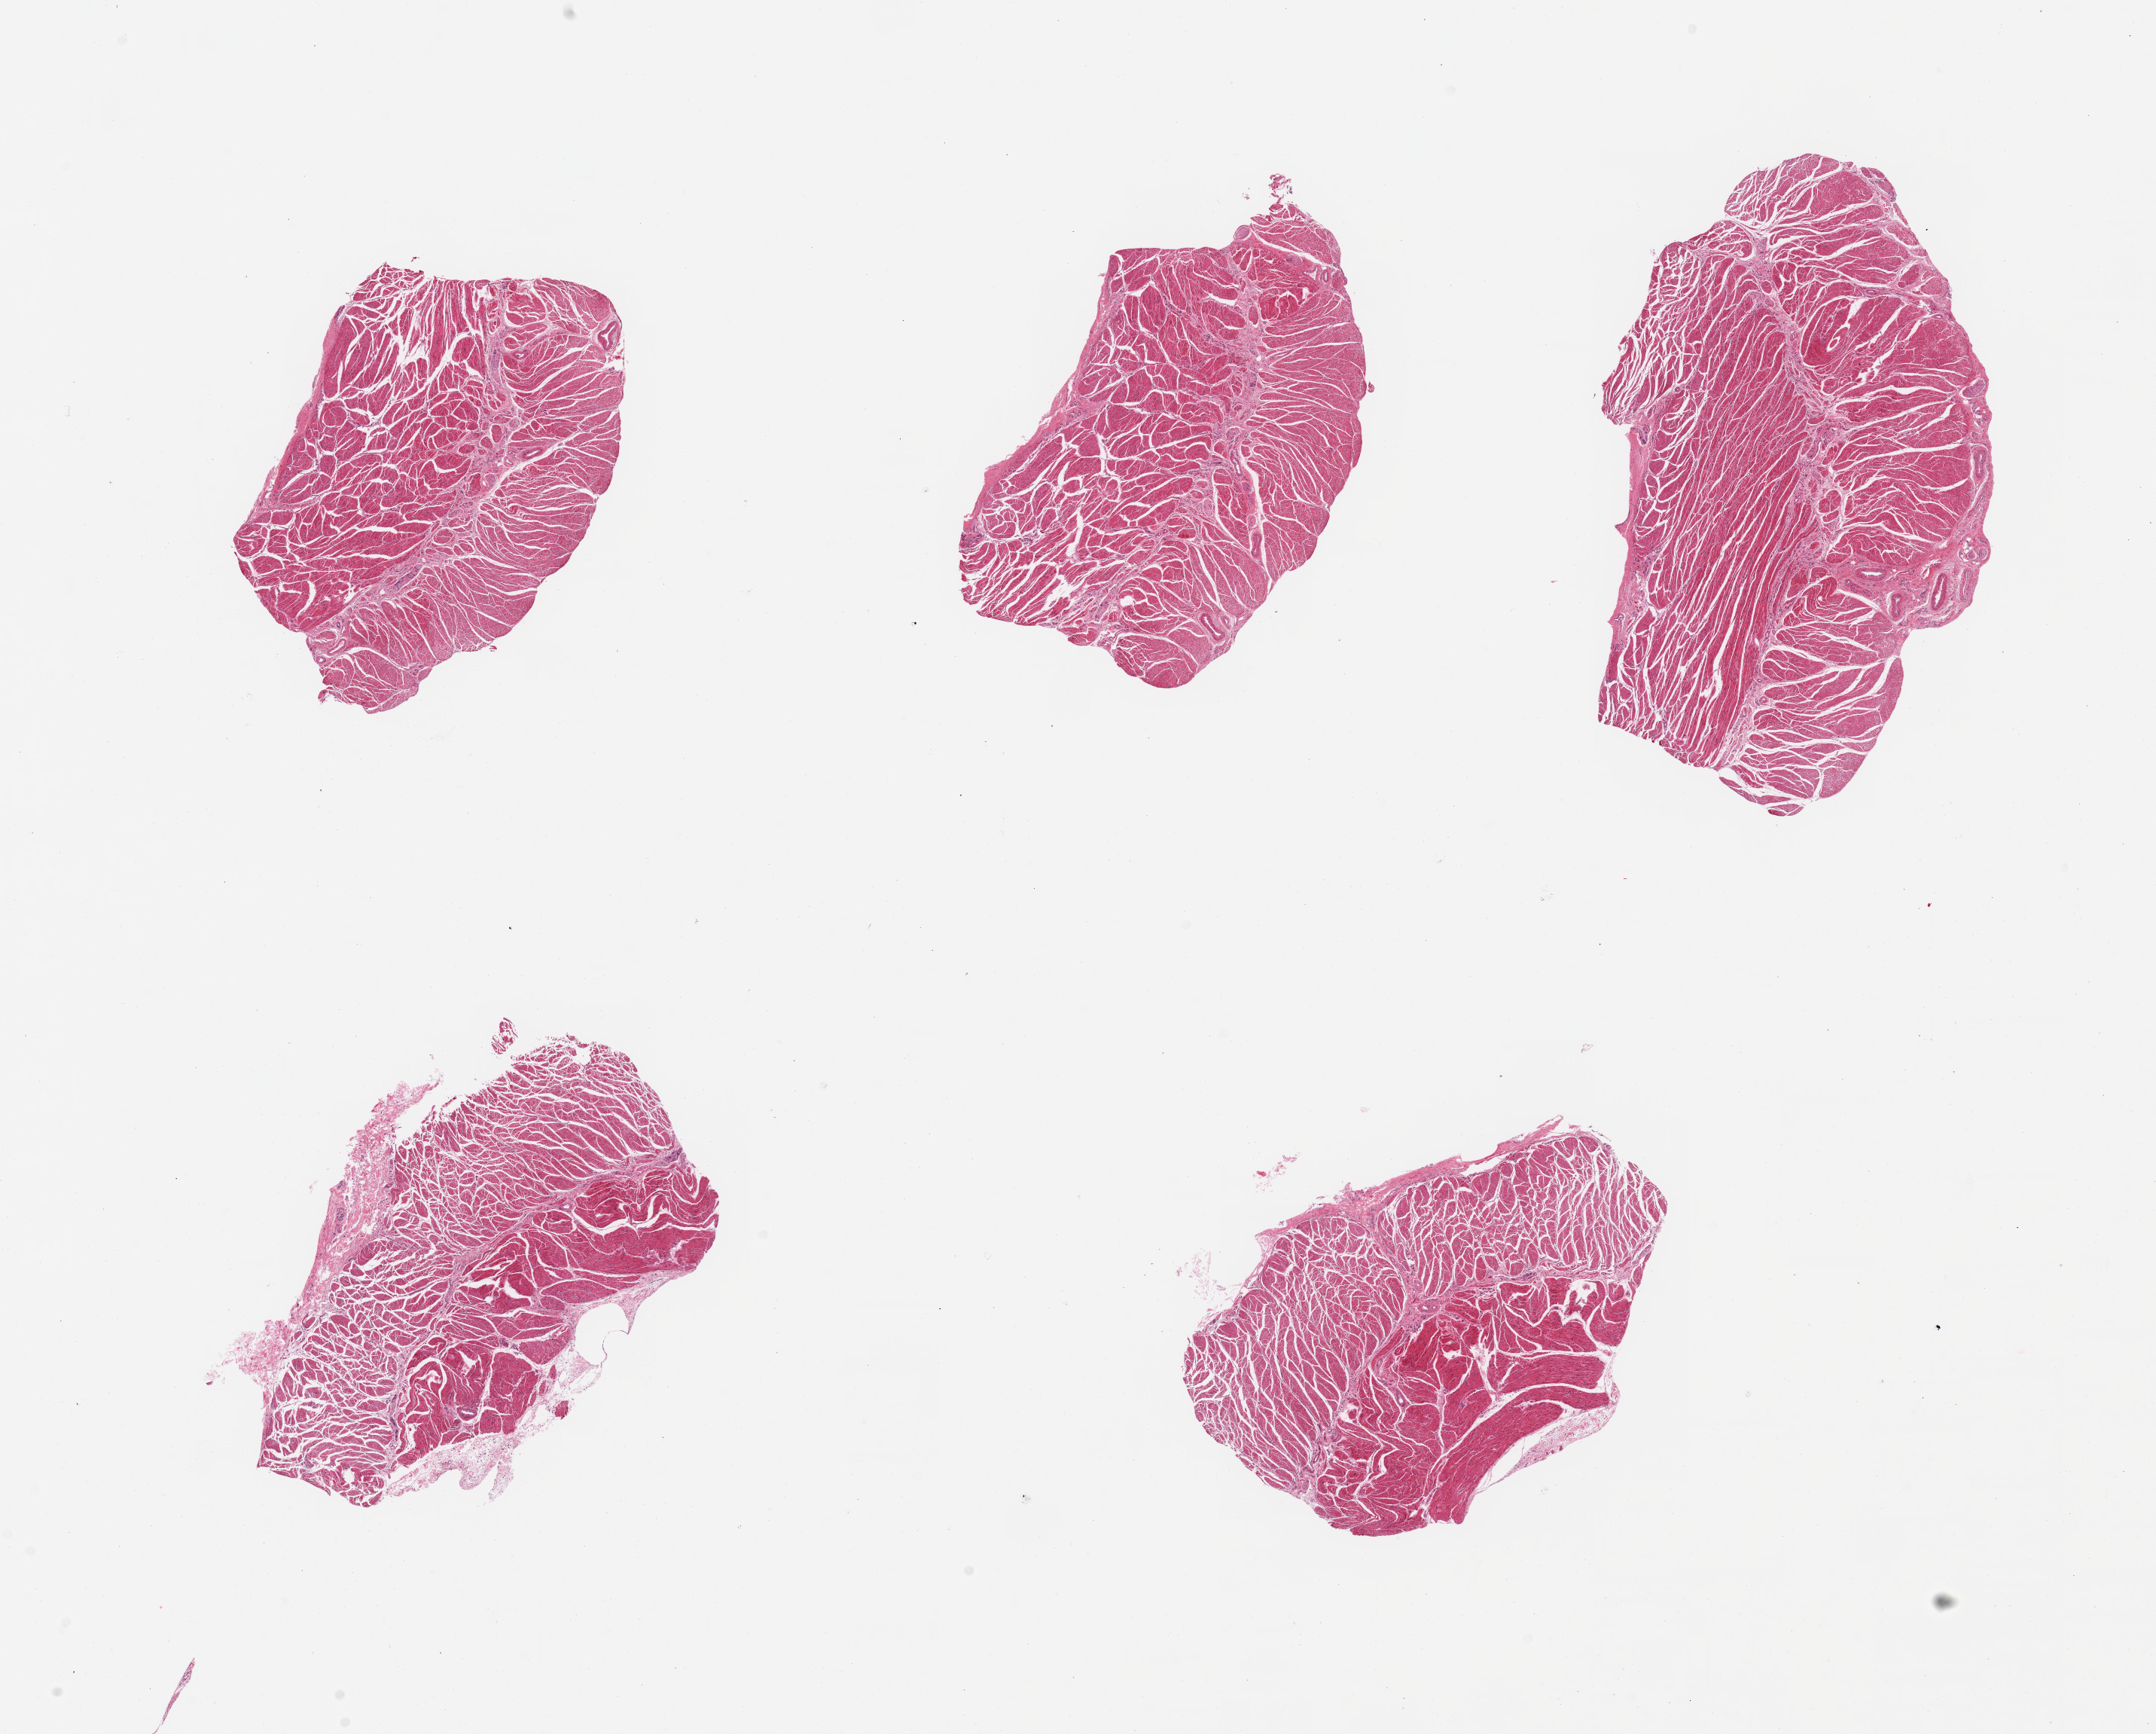
Digitized hematoxylin and eosin (H&E)-stained section — whole scanned area (about 22.6 x 18.2 mm) shown as a low-resolution overview; PAXgene-fixed, paraffin-embedded tissue; section of esophageal muscle (target tissue); tissue donor sample. Female donor.
• review note (as recorded): 6 pieces; well trimmed target muscularis